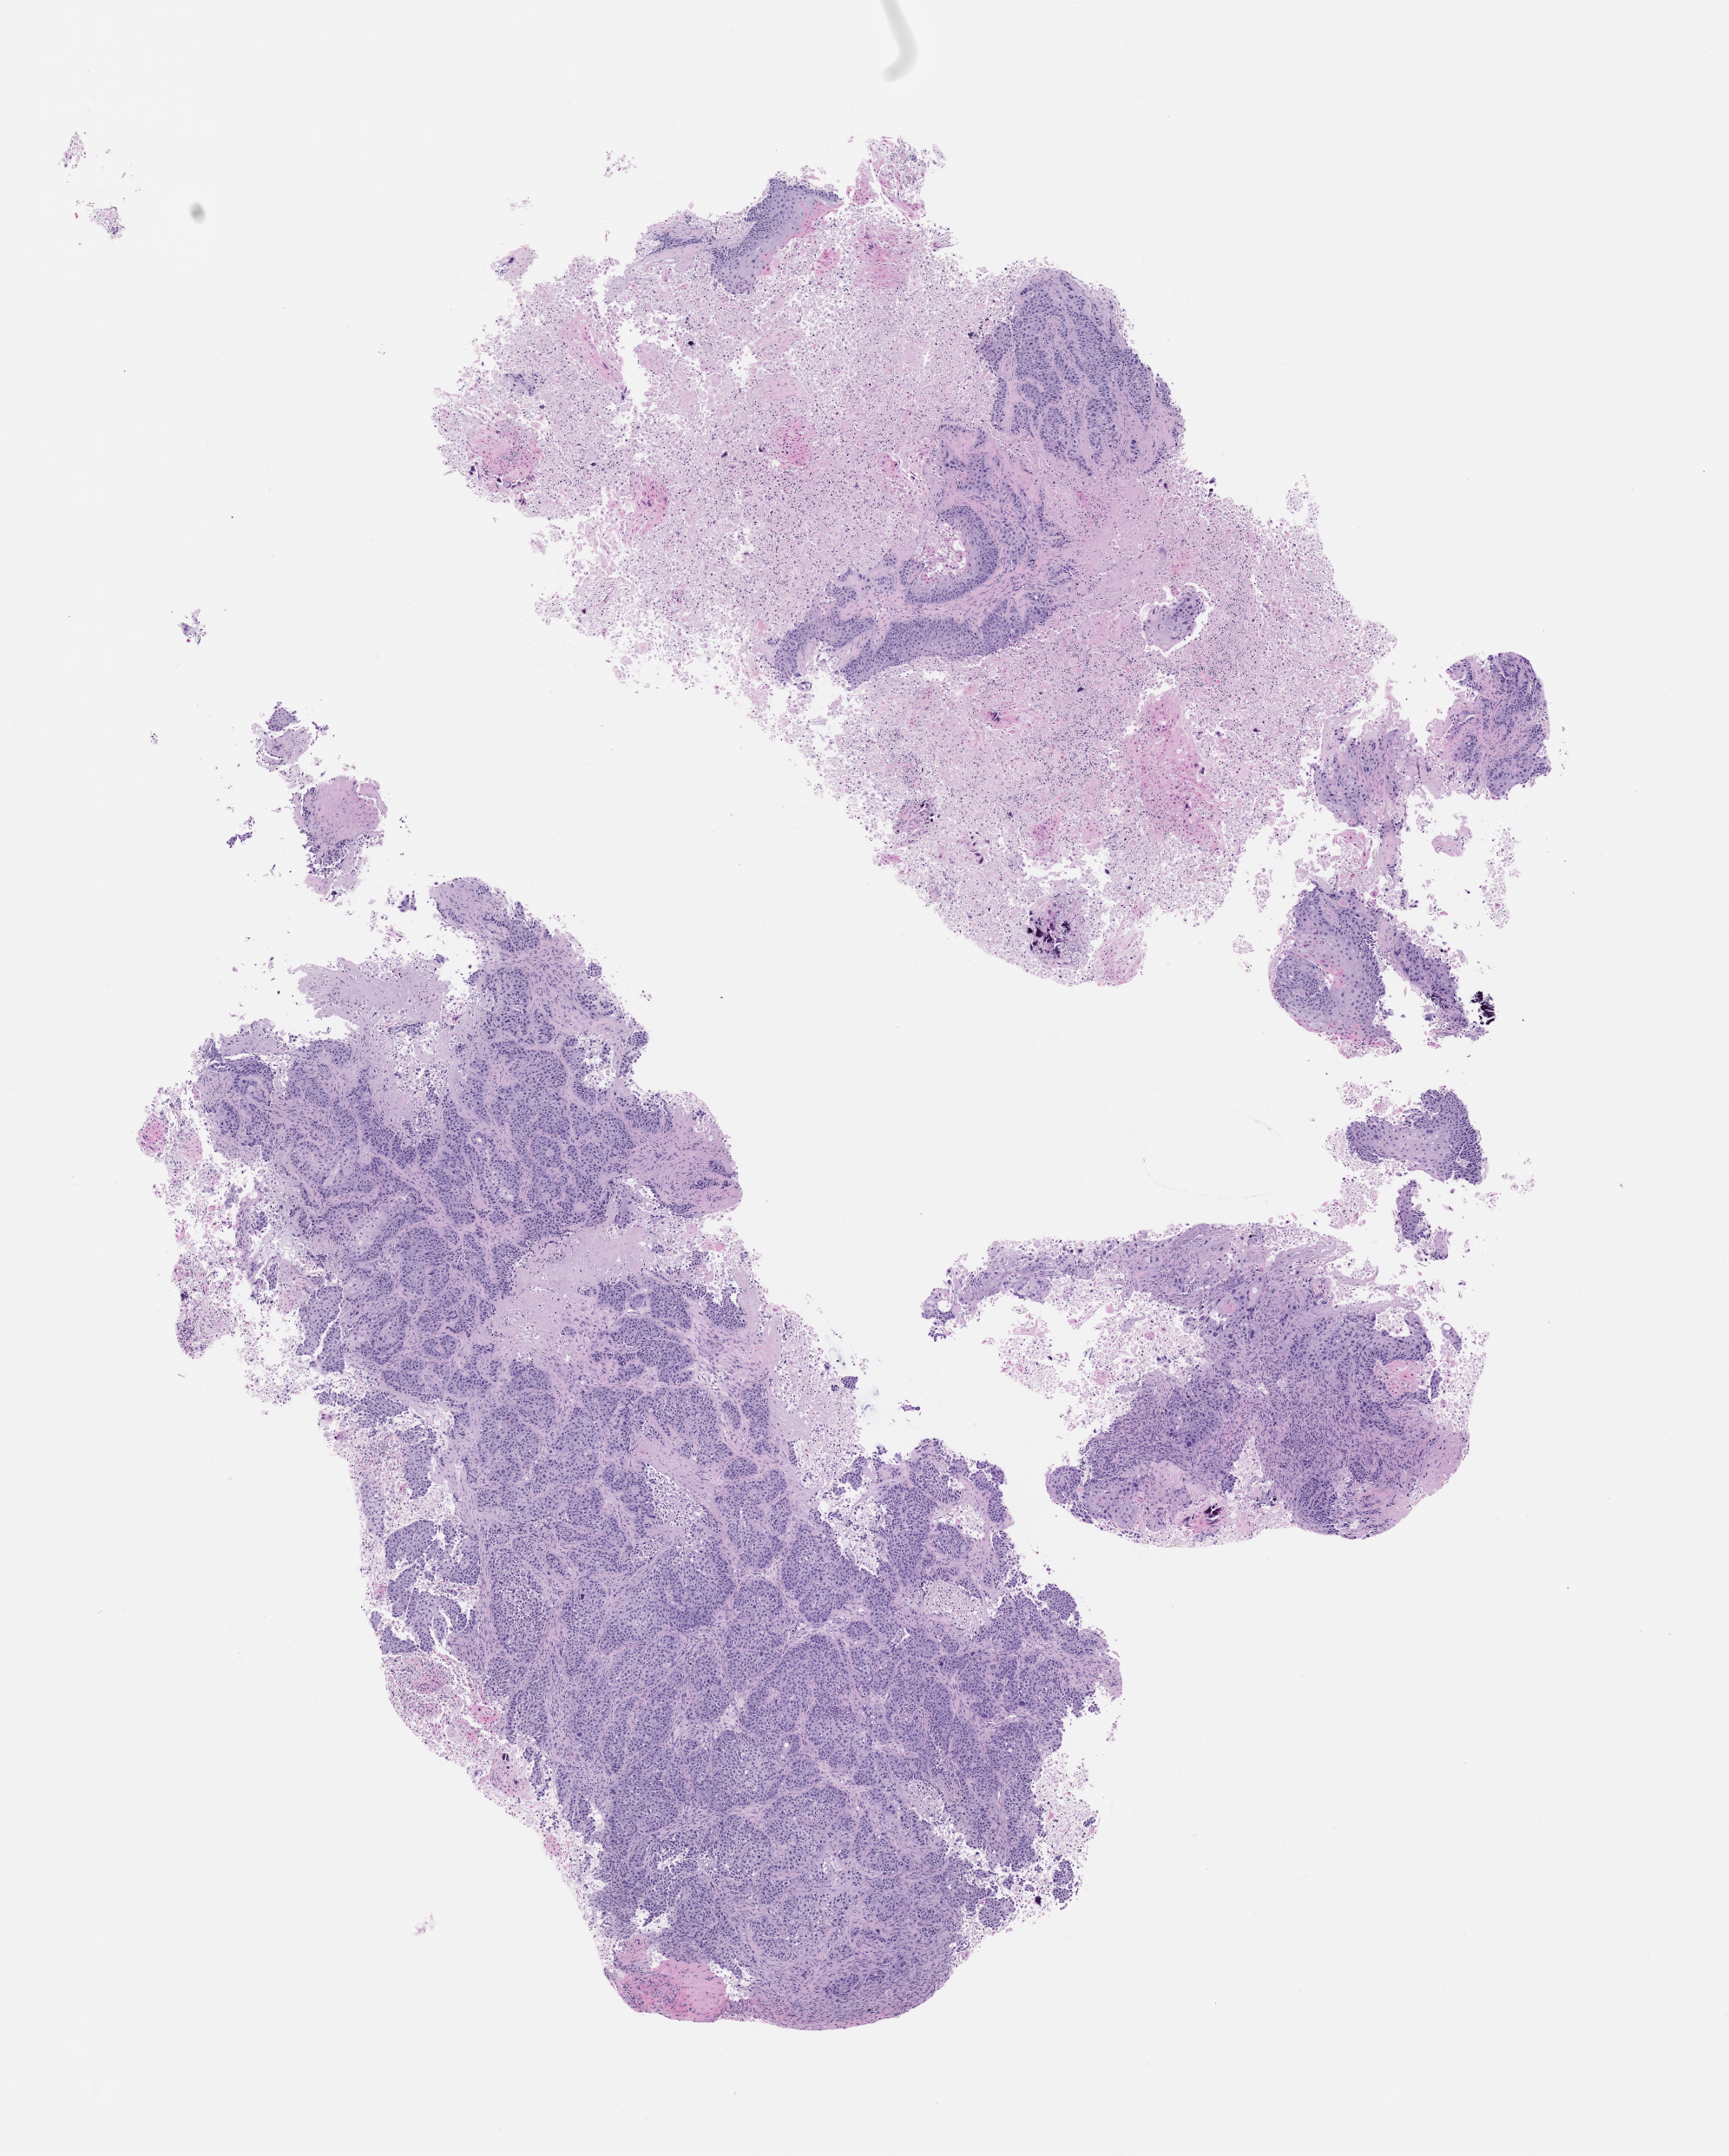
H&E whole-slide image of a patient-derived xenograft (PDX) tumor grown in a mouse, passage 0, shown as a low-resolution overview of the whole scanned area (about 8.0 x 10.0 mm). FFPE section. Originating tumor site category: lung.
- originating patient diagnosis: Lung Squamous Cell Carcinoma